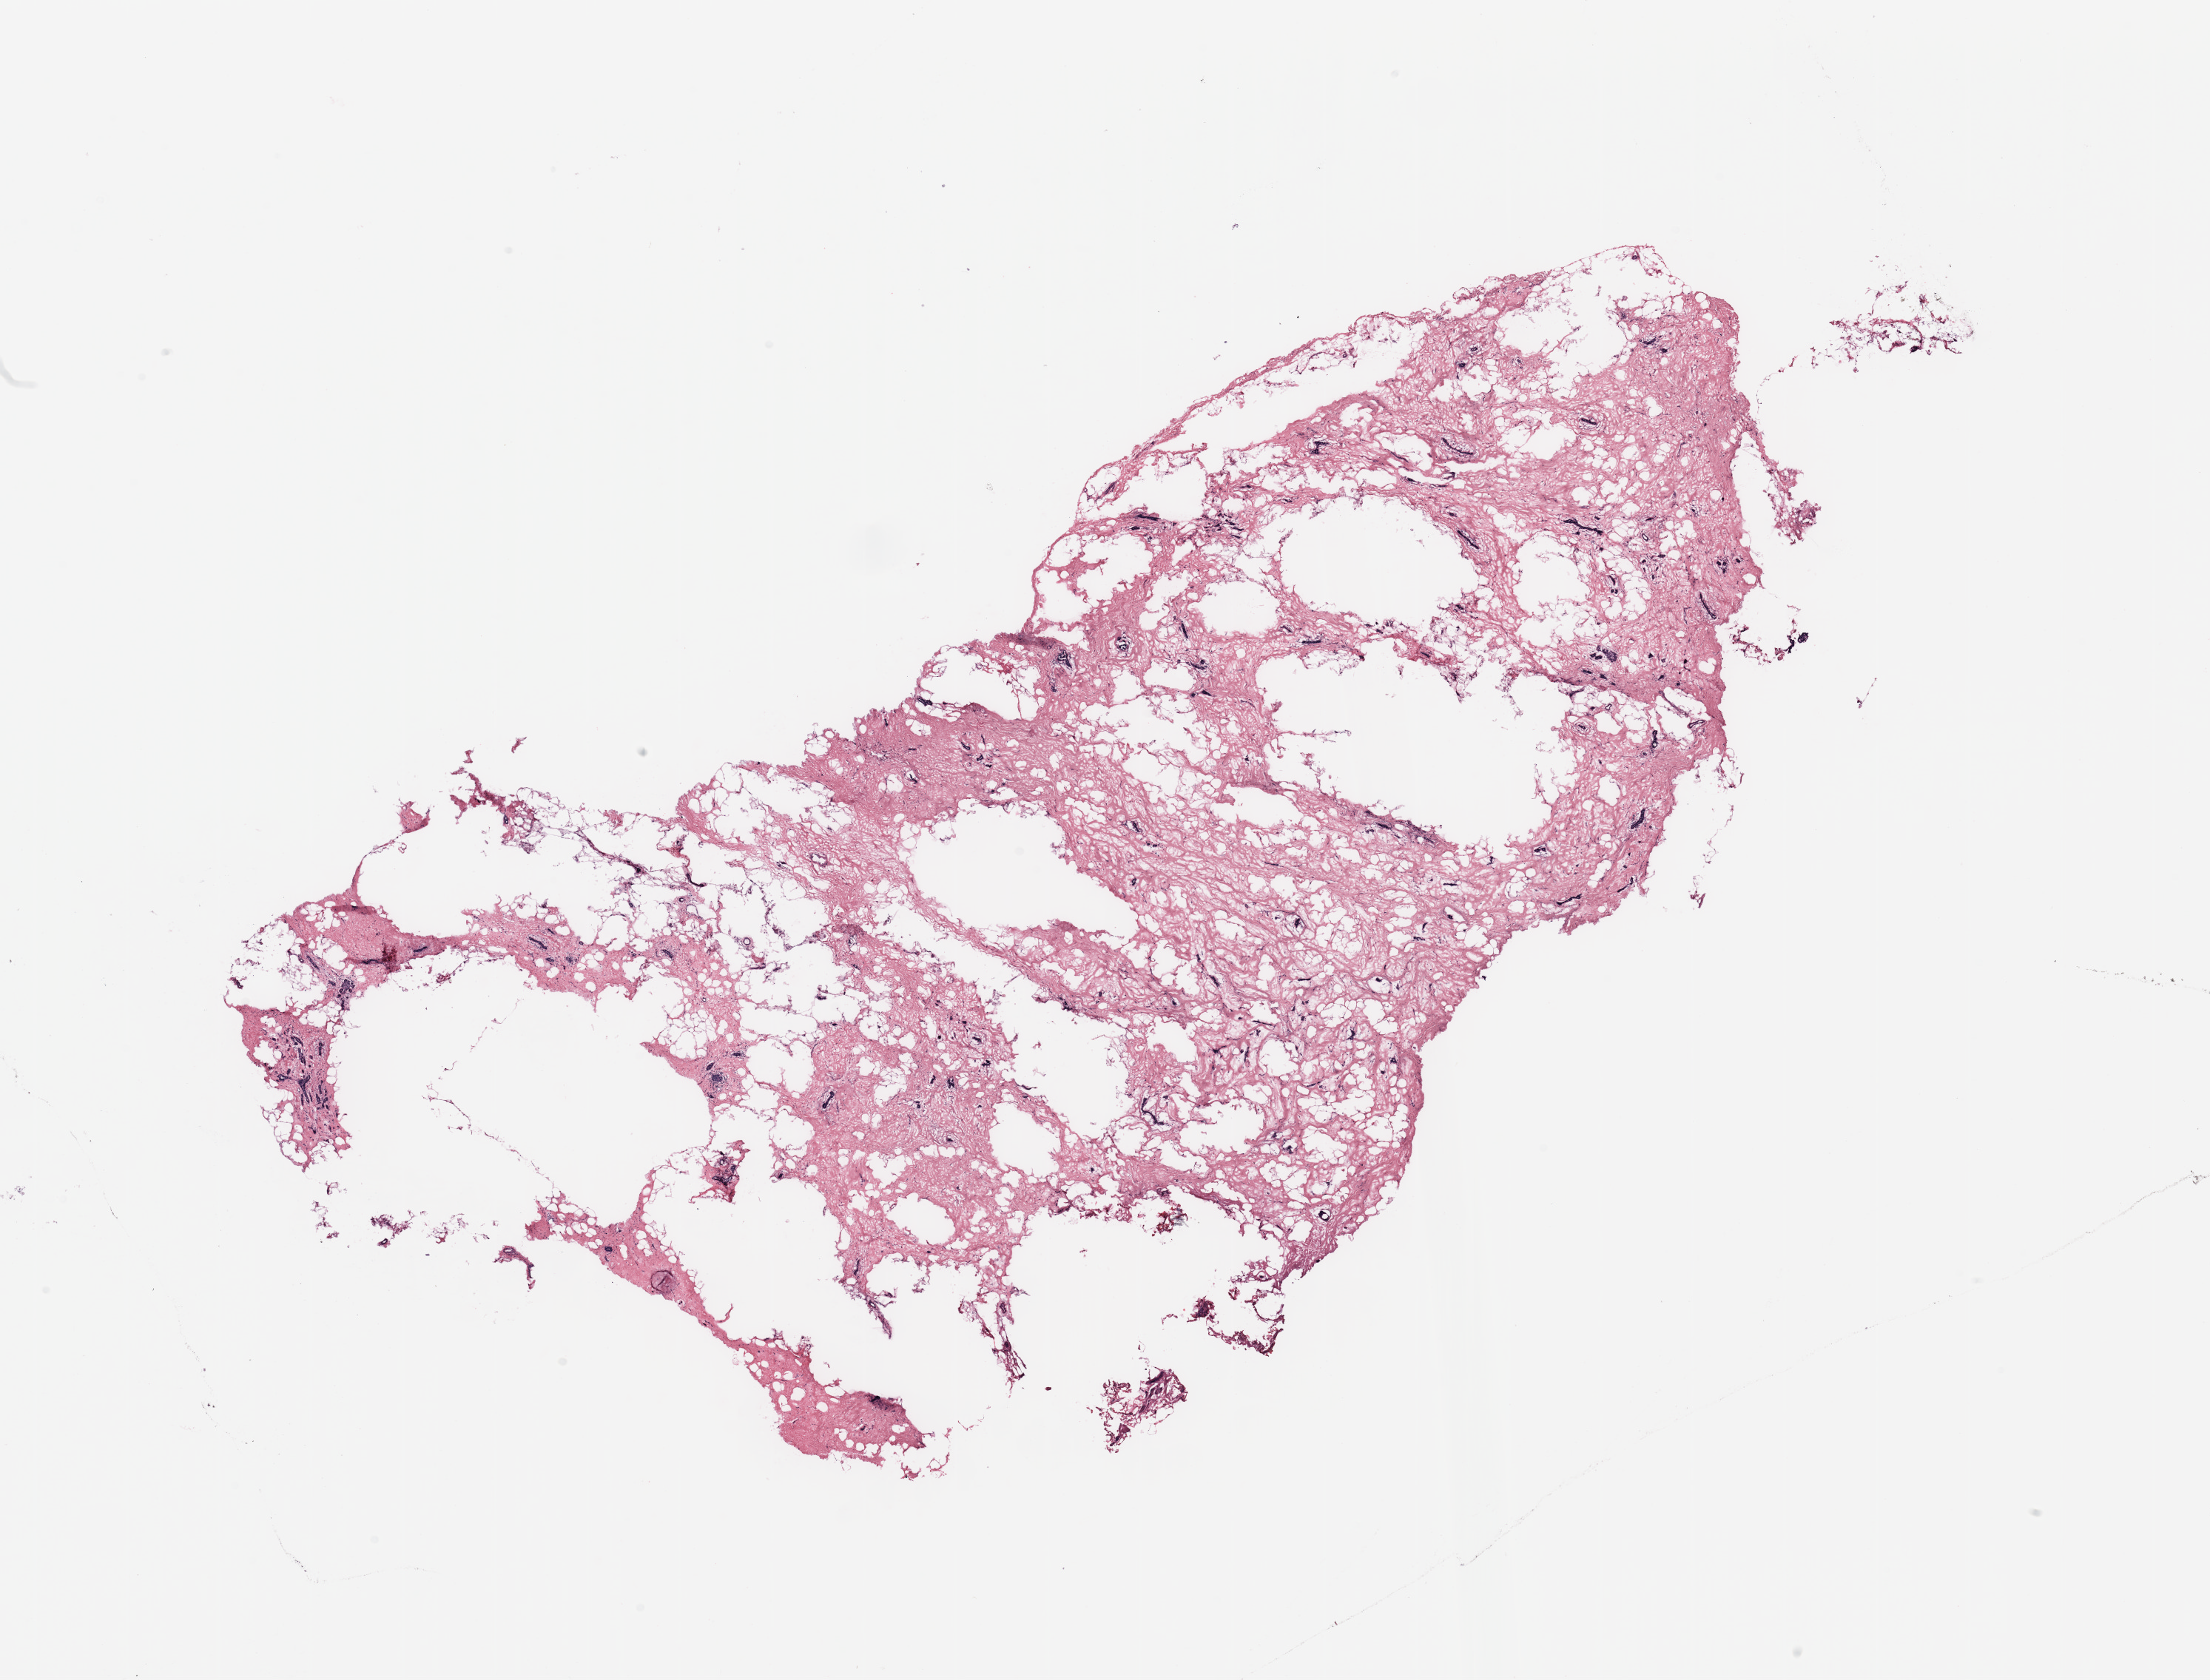
Whole-slide histology image, H&E, whole scanned area (about 23.6 x 18.0 mm) shown as a low-resolution overview. Breast, tissue type not recorded.
Patient diagnosis (cohort enrolment): breast cancer (breast).